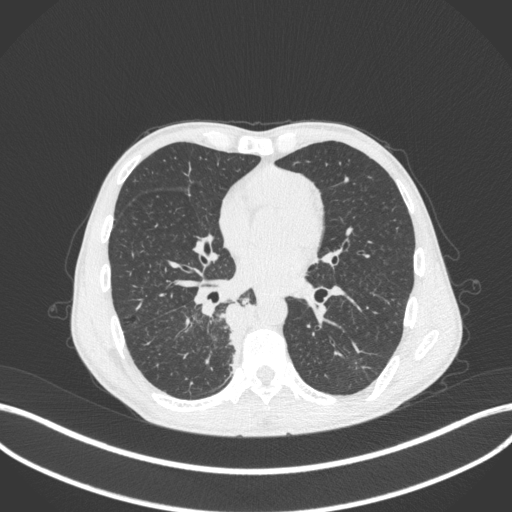
Chest CT, one axial slice. Position 177 of 371 along the scan axis. Reconstruction kernel B31f. 120 kVp. Lung window (W 1500 / L -600 HU). 1 mm slice thickness. 512 × 512 image matrix. Patient: male, 58 years. From the clinical record (not read from this slice): clinical TNM (as recorded): T3 N1 M1.
Annotated regions visible in this slice (rectangle marked by the reading radiologist):
- lung tumour (recorded histology: squamous cell carcinoma): bounding box <221,300,258,366> (left, top, right, bottom; pixels)